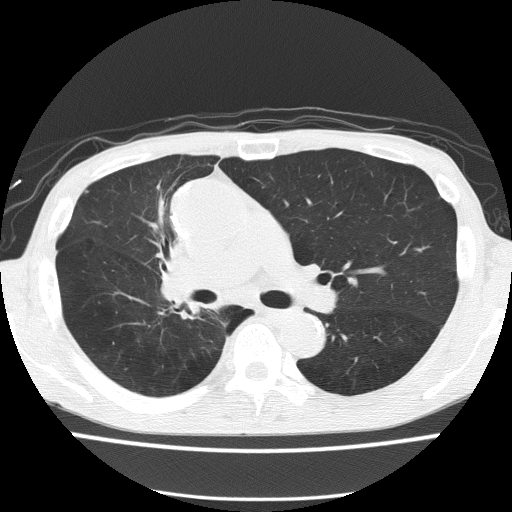
Low-dose screening chest CT, axial slice. First (baseline) screen. Lung window (W 1500 / L -600 HU). 2 mm slice thickness. Lung (sharp) reconstruction kernel (FC51). 120 kVp. 512 × 512 image matrix. Male participant, aged 59 years at enrolment. Former smoker at enrolment.
Expert-annotated lung lesion, box from (x=143, y=229) to (x=231, y=321) px. The screening reader recorded 5 non-calcified nodules or masses ≥4 mm on this exam; which of them this box marks is not recorded. Official screen result: positive, change unspecified: nodule(s) >= 4 mm or enlarging nodule(s), mass(es), or other non-specific abnormalities suspicious for lung cancer. Lung cancer was diagnosed 72 days after this screen: squamous cell carcinoma, NOS, right upper lobe, moderately differentiated (G2), stage IV (AJCC 6th edition).